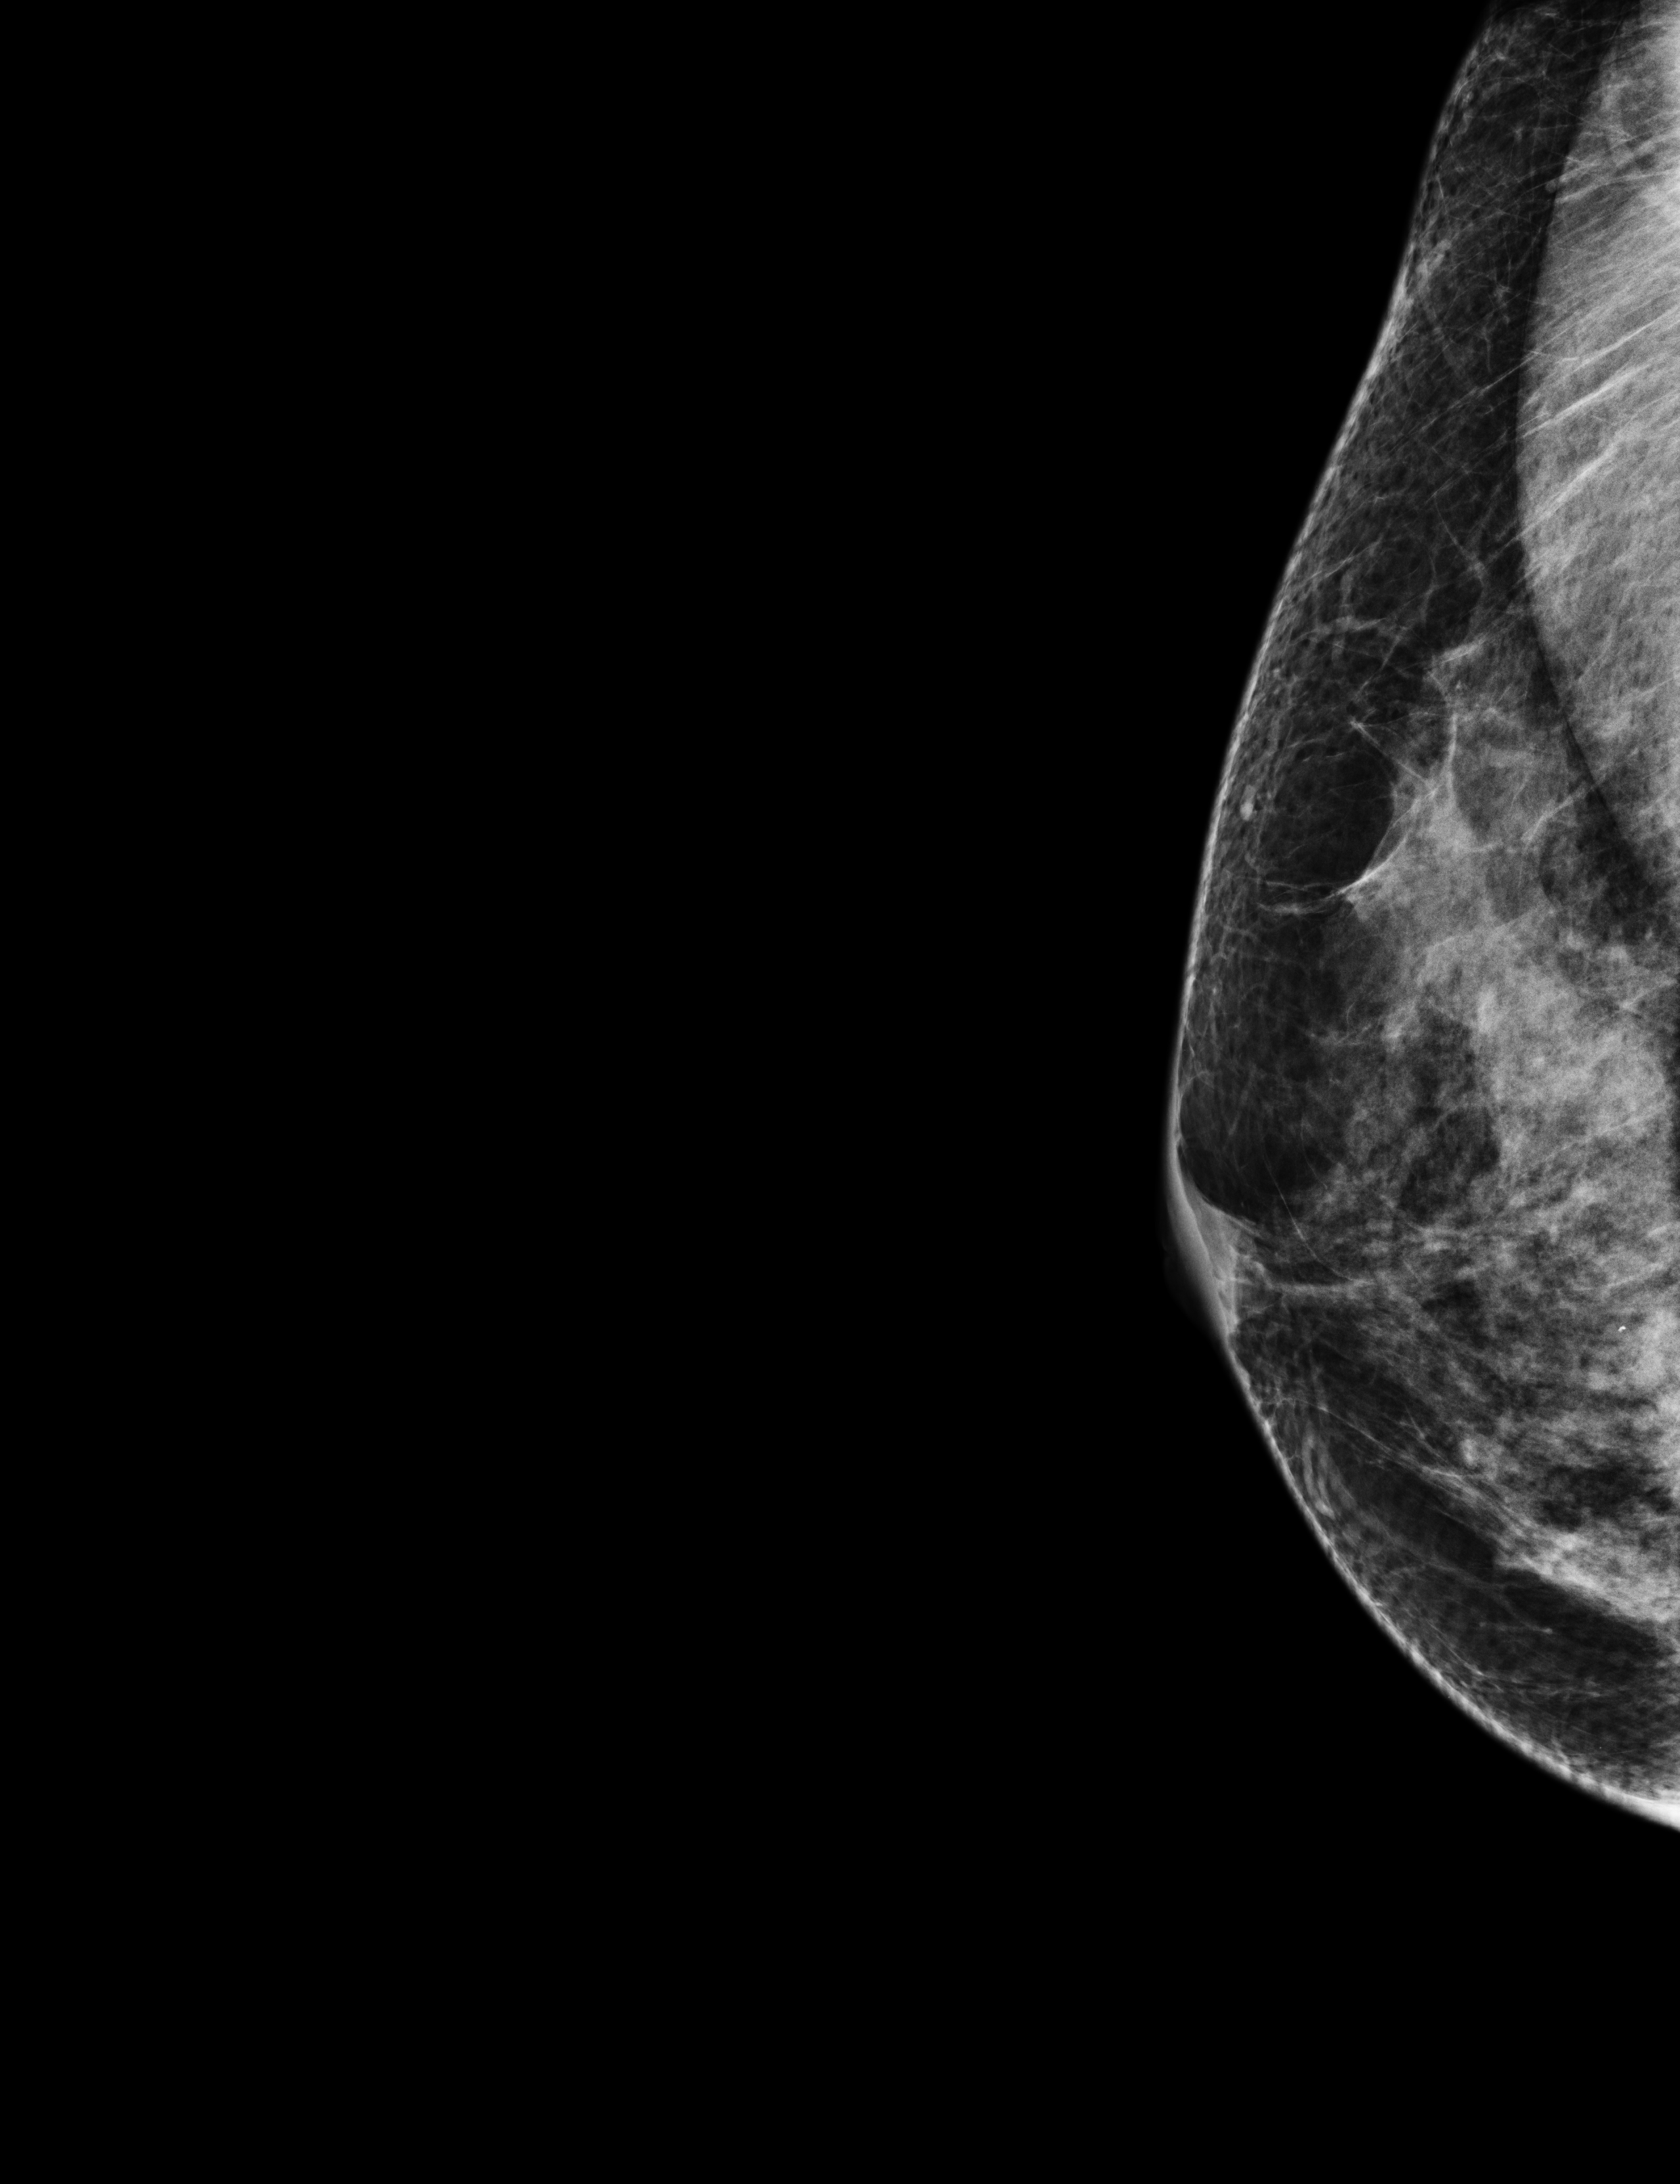
Full-field digital mammogram (FFDM); right breast; laterally exaggerated craniocaudal (XCCL) view; annual screening mammography examination. Female patient, age 41 years.
BI-RADS breast density category at the screening exam (both breasts, scale 1–4): 4. Final BI-RADS assessment for this screening round (tomosynthesis exam, both breasts): category 1. Recall: no recall after this screen.